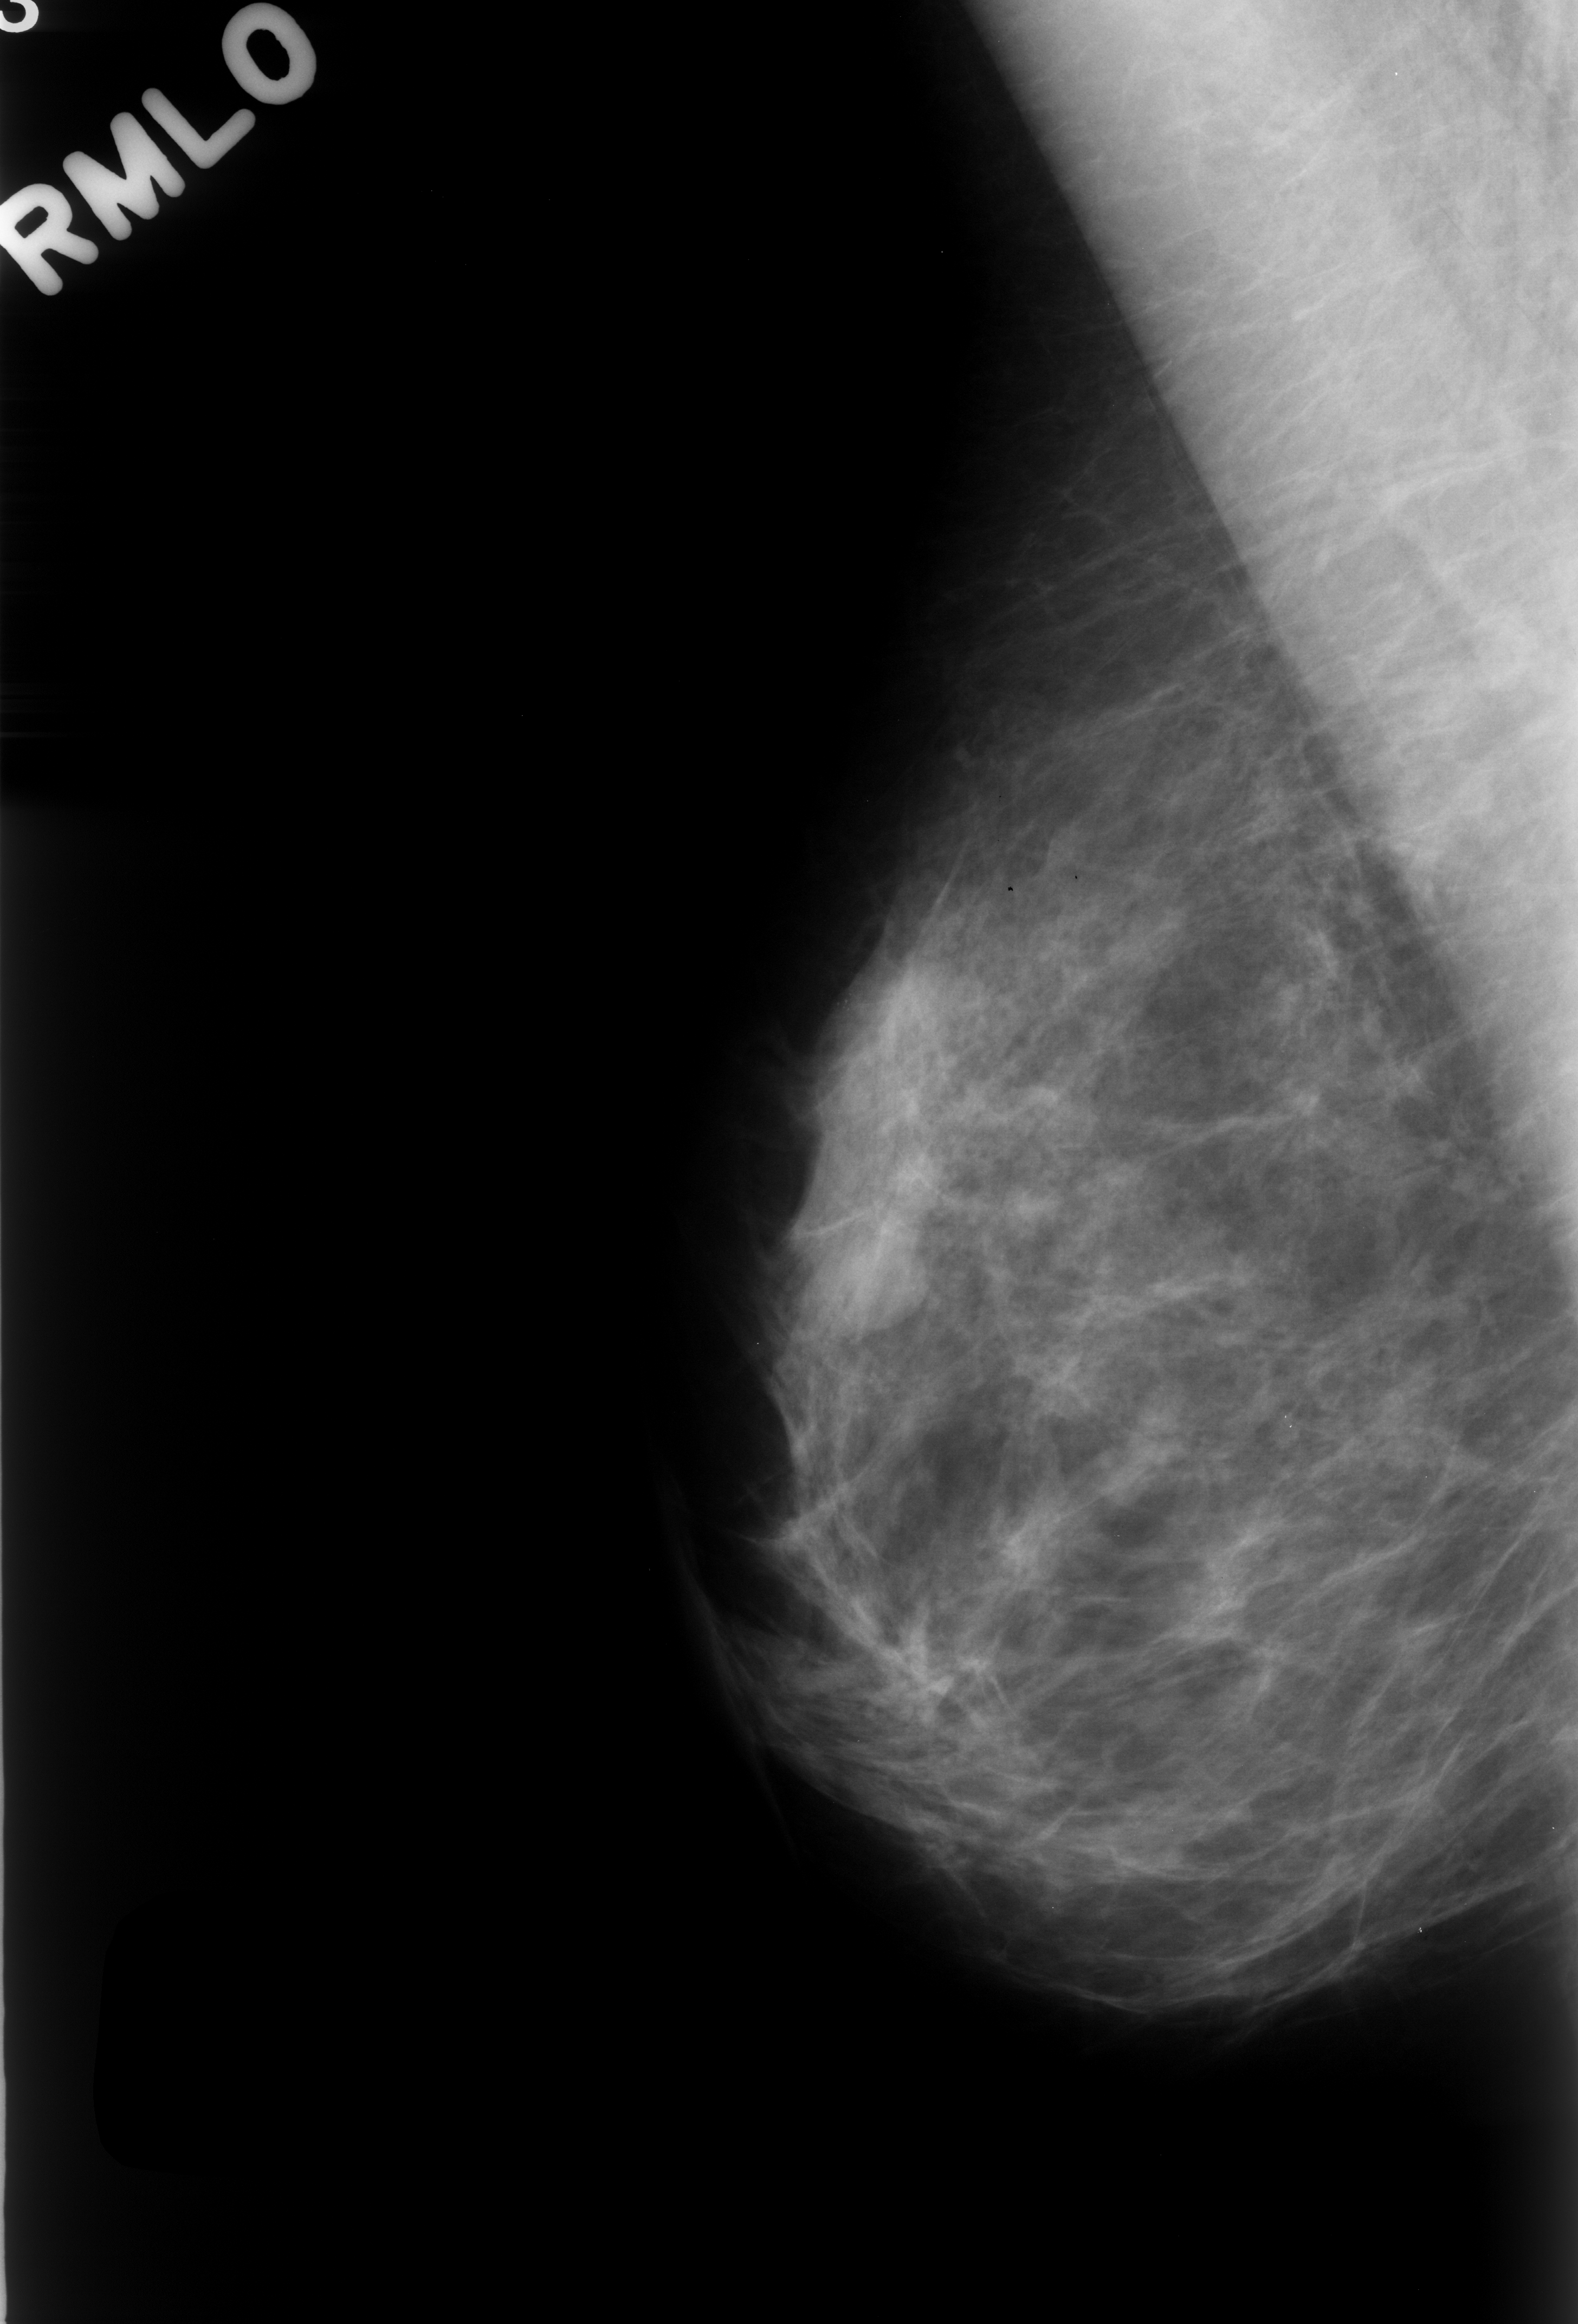
Scanned film-screen mammogram; right breast; mediolateral oblique (MLO) view; BI-RADS breast density category 2 (scale 1–4); 1578 × 2324 image matrix.
Marked abnormalities (boxes around the expert regions of interest):
- mass, shape oval, margins circumscribed; BI-RADS assessment category 3; subtlety rating 4 on a 1 (subtle) to 5 (obvious) scale; pathology (as recorded): benign: bounding box [x1, y1, x2, y2] px = [779, 1186, 940, 1338]